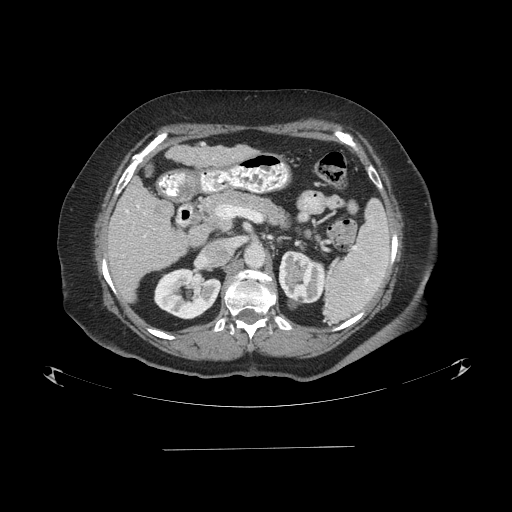
Contrast-enhanced abdominal CT (liver protocol), one axial slice. Slice 42 of 103 in the series (ordered by position). 120 kVp. One of 2 acquisitions stored at this slice position. Soft-tissue window (W 400 / L 40 HU). 2.5 mm slice thickness. 512 × 512 image matrix, field of view 500 × 500 mm. Case-level facts recorded for this patient, not image findings: diagnosis: hepatocellular carcinoma (patient treated with transarterial chemoembolisation; whether this scan precedes or follows treatment is not stated here); TNM stage (as recorded): Stage-IIIA; Child-Pugh class: A; tumour differentiation: poorly differentiated; tumour nodularity: multinodular.
Structures marked on this image (semi-automatic segmentation, software-assisted and operator-edited):
- liver parenchyma outside the tumour (the mass and vessels are separate outlines, so this box may not span the whole liver): bounding box <106,178,192,298> (left, top, right, bottom; pixels)
- liver vessels: <125,205,145,237>